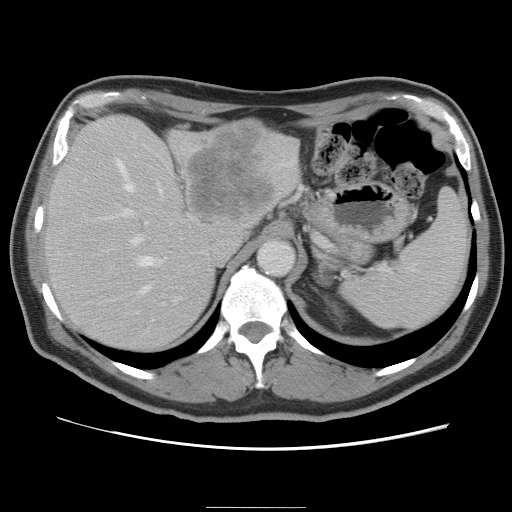
Contrast-enhanced abdominal CT, one axial slice; slice 57 of 87 in the series (ordered by position); intravenous contrast given; soft-tissue window (W 400 / L 40 HU); 512 × 512 image matrix. Male patient, age 63 years. From the clinical record (not read from this slice): diagnosis: colorectal cancer liver metastases, imaged before liver resection; multiple liver metastases: no; largest metastasis: 9 cm; chemotherapy before resection: no.
Annotated regions visible in this slice (expert manual segmentation):
- hepatic veins: bounding box [x1, y1, x2, y2] px = [113, 159, 167, 322]
- liver: [43, 116, 302, 353]
- planned liver remnant (the part of the liver to remain after resection): [43, 152, 216, 353]
- portal vein (with intrahepatic branches): [97, 208, 192, 314]
- liver metastasis: [188, 125, 272, 218]